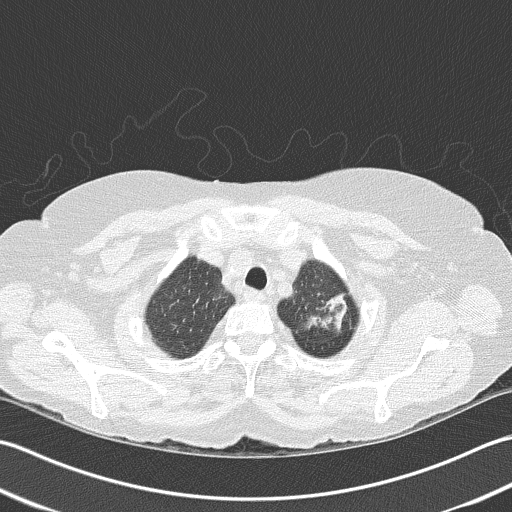
Axial slice from a low-dose chest CT screening exam; baseline annual screen; lung window (W 1500 / L -600 HU); lung (sharp) reconstruction kernel (B50f); slice 138 of 159 in the series. Female, age 68 years at enrolment. Former smoker at enrolment.
Lesion marked by an expert reader, bounding box [x1, y1, x2, y2] px = [290, 274, 363, 341]. No non-calcified nodule or mass ≥4 mm was recorded by the screening reader at this exam.